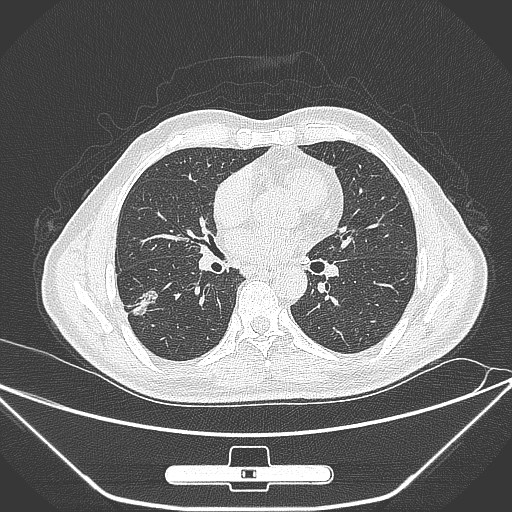
Chest CT, one axial slice. Slice 142 of 309 in the series (ordered by position). Lung window (W 1500 / L -600 HU). 1 mm slice thickness. 512 × 512 image matrix, field of view 398 × 398 mm. Male patient, age 71 years. From the clinical record (not read from this slice): clinical TNM (as recorded): T1c N0 M0.
Annotated regions visible in this slice (rectangle marked by the reading radiologist):
- lung tumour (recorded histology: adenocarcinoma): box from (x=126, y=289) to (x=169, y=332) px